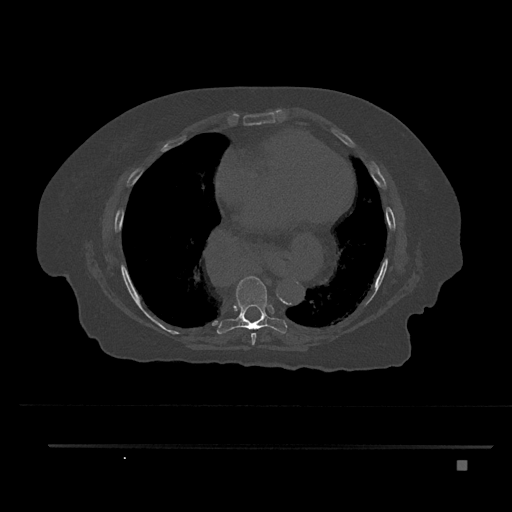
CT including the spine, one axial slice. Position 449 of 797 along the scan axis. Reconstruction kernel Br40s/3. Bone window (W 1800 / L 400 HU). 512 × 512 image matrix. Patient: female, 76 years. From the clinical record (not read from this slice): primary cancer: lung.
Structures marked on this image (semi-automatically segmented with operator editing):
- T7 vertebra: bounding box (x1, y1, x2, y2) in pixels: (251, 333, 256, 346)
- T8 vertebra: (217, 276, 287, 334)